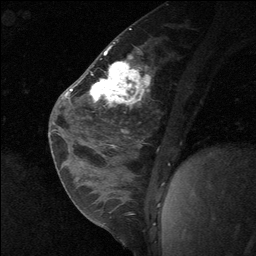
Breast MRI (dynamic contrast-enhanced), one sagittal slice; dynamic contrast-enhanced study with each time point stored as its own series, time point 2 of 3 at this slice position (early post-contrast, ordered by acquisition time); 1.5 T; TE 4.8 ms, TR 27 ms; 2 mm slice thickness; 256 × 256 image matrix. Patient: female, 26 years. From the clinical record (not read from this slice): setting: breast cancer imaged before/during neoadjuvant chemotherapy; receptor status: HR-positive, HER2-negative.
Structures marked on this image (semi-automatic segmentation, software-assisted and operator-edited):
- analysis volume of interest (the breast-tissue region the enhancement analysis was run in; not a lesion): bounding box (x1, y1, x2, y2) in pixels: (86, 43, 133, 138)
- tumour enhancement mask (voxels above the 90 % enhancement threshold inside the analysis volume of interest): (90, 64, 125, 102)